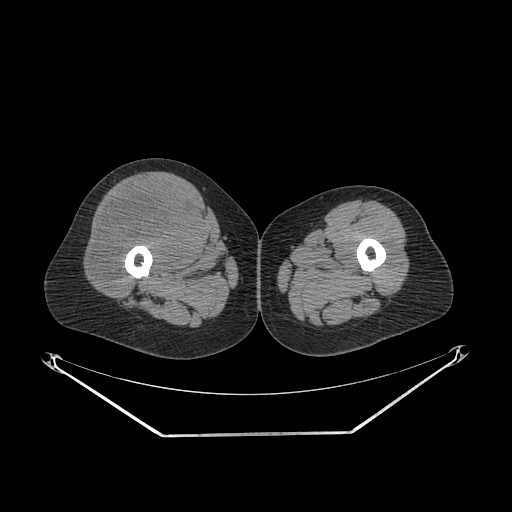
CT of an extremity soft-tissue mass (from a PET/CT study), one axial slice; position 248 of 311 along the scan axis; reconstruction kernel SOFT; 140 kVp; soft-tissue window (W 400 / L 40 HU); 3.75 mm slice thickness; 512 × 512 image matrix, field of view 500 × 500 mm. Female patient. From the clinical record (not read from this slice): histological type: pleiomorphic undifferentiated sarcoma; grade: high; site of the primary tumour: right quadricep.
Annotated regions visible in this slice (expert contour drawn on MRI and transferred to this co-registered scan by the dataset authors):
- tumour plus oedema (research contour): bounding box [x1, y1, x2, y2] px = [94, 185, 197, 286]
- tumour (research contour): [94, 185, 197, 286]